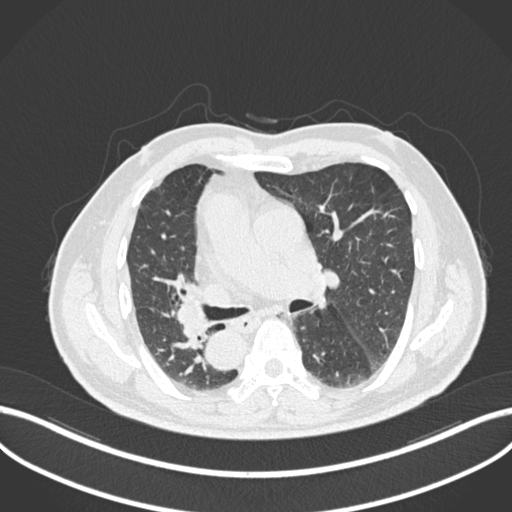
Chest CT, one axial slice; slice 124 of 206 in the series (ordered by position); 120 kVp; lung window (W 1500 / L -600 HU); 512 × 512 image matrix, field of view 400 × 400 mm. Male patient, age 67 years. From the clinical record (not read from this slice): clinical TNM (as recorded): T2a N0 M0.
Annotated regions visible in this slice (rectangle marked by the reading radiologist):
- lung tumour (recorded histology: squamous cell carcinoma): bounding box (x1, y1, x2, y2) in pixels: (174, 293, 217, 351)